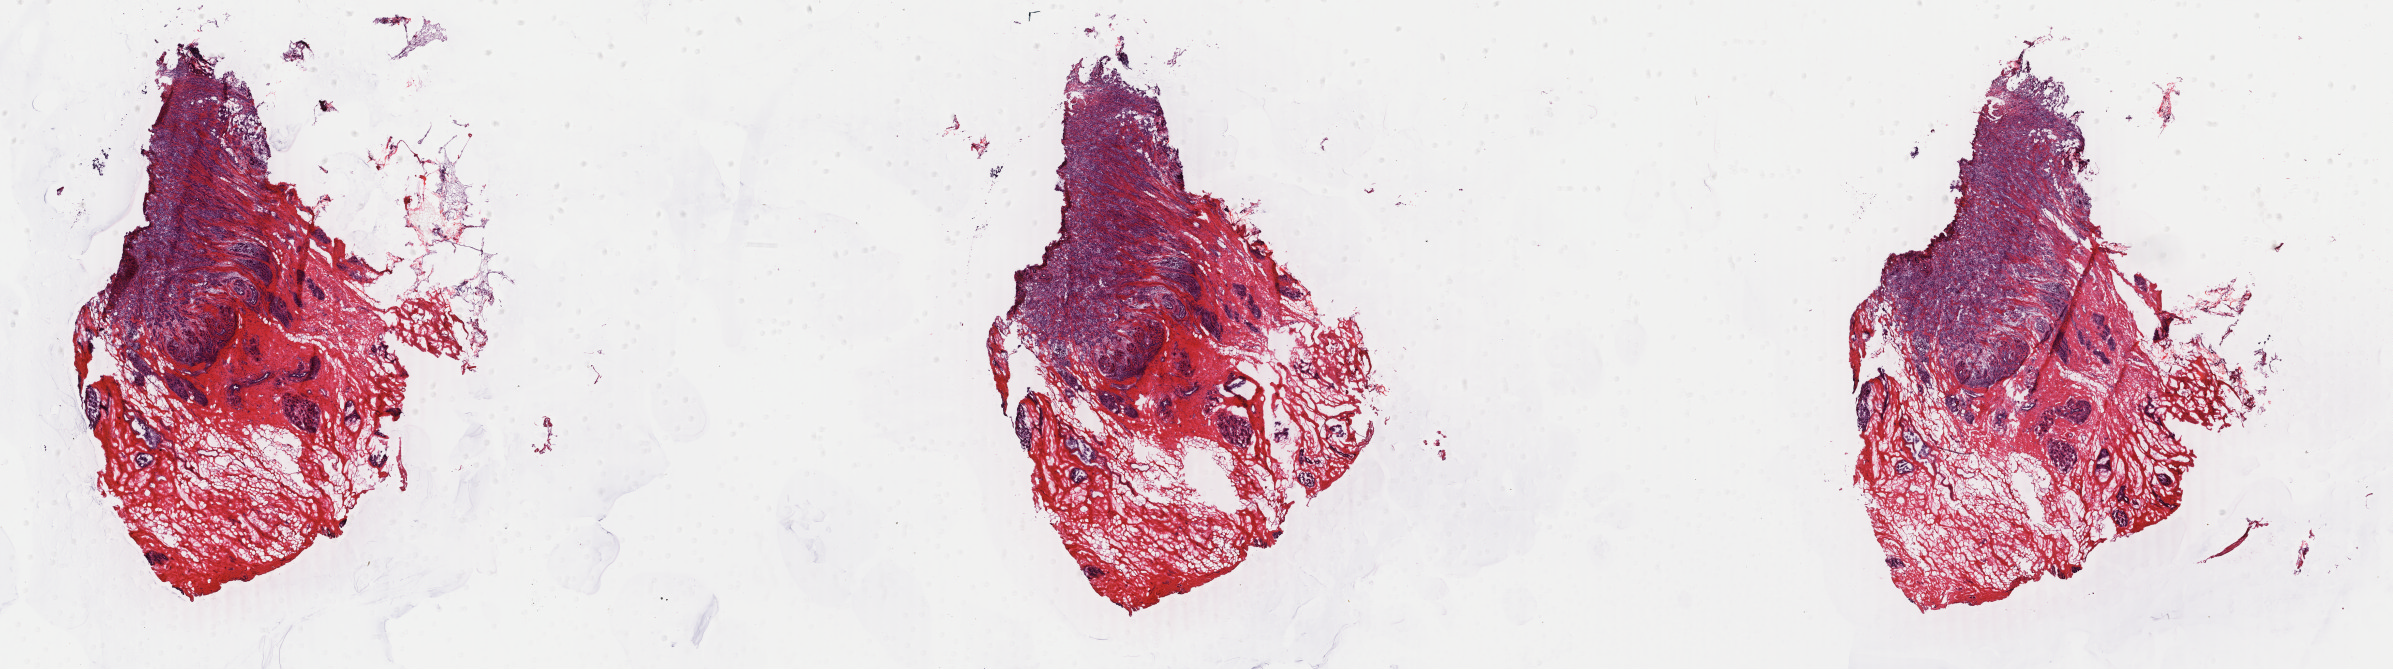
Digitized H&E tissue section (whole slide) — a low-resolution overview of the entire scanned area, about 38.1 x 10.6 mm (acquisition: 40x scan); frozen section from the bottom of the tissue portion; sample: primary tumour, breast. Female patient; age at initial diagnosis 46 years. Composition of this section per pathologist review: tumour cells 40%, tumour nuclei 85%, normal cells 60%, stromal cells 0%, necrosis 0%. Inflammatory infiltration, as recorded: lymphocyte infiltration 0%, monocyte infiltration 0%, neutrophil infiltration 0%.
• lymph nodes positive (case pathology): 0 of 2 examined
• diagnosis: Infiltrating duct carcinoma, NOS
• AJCC pathologic stage: IIA (6th edition)